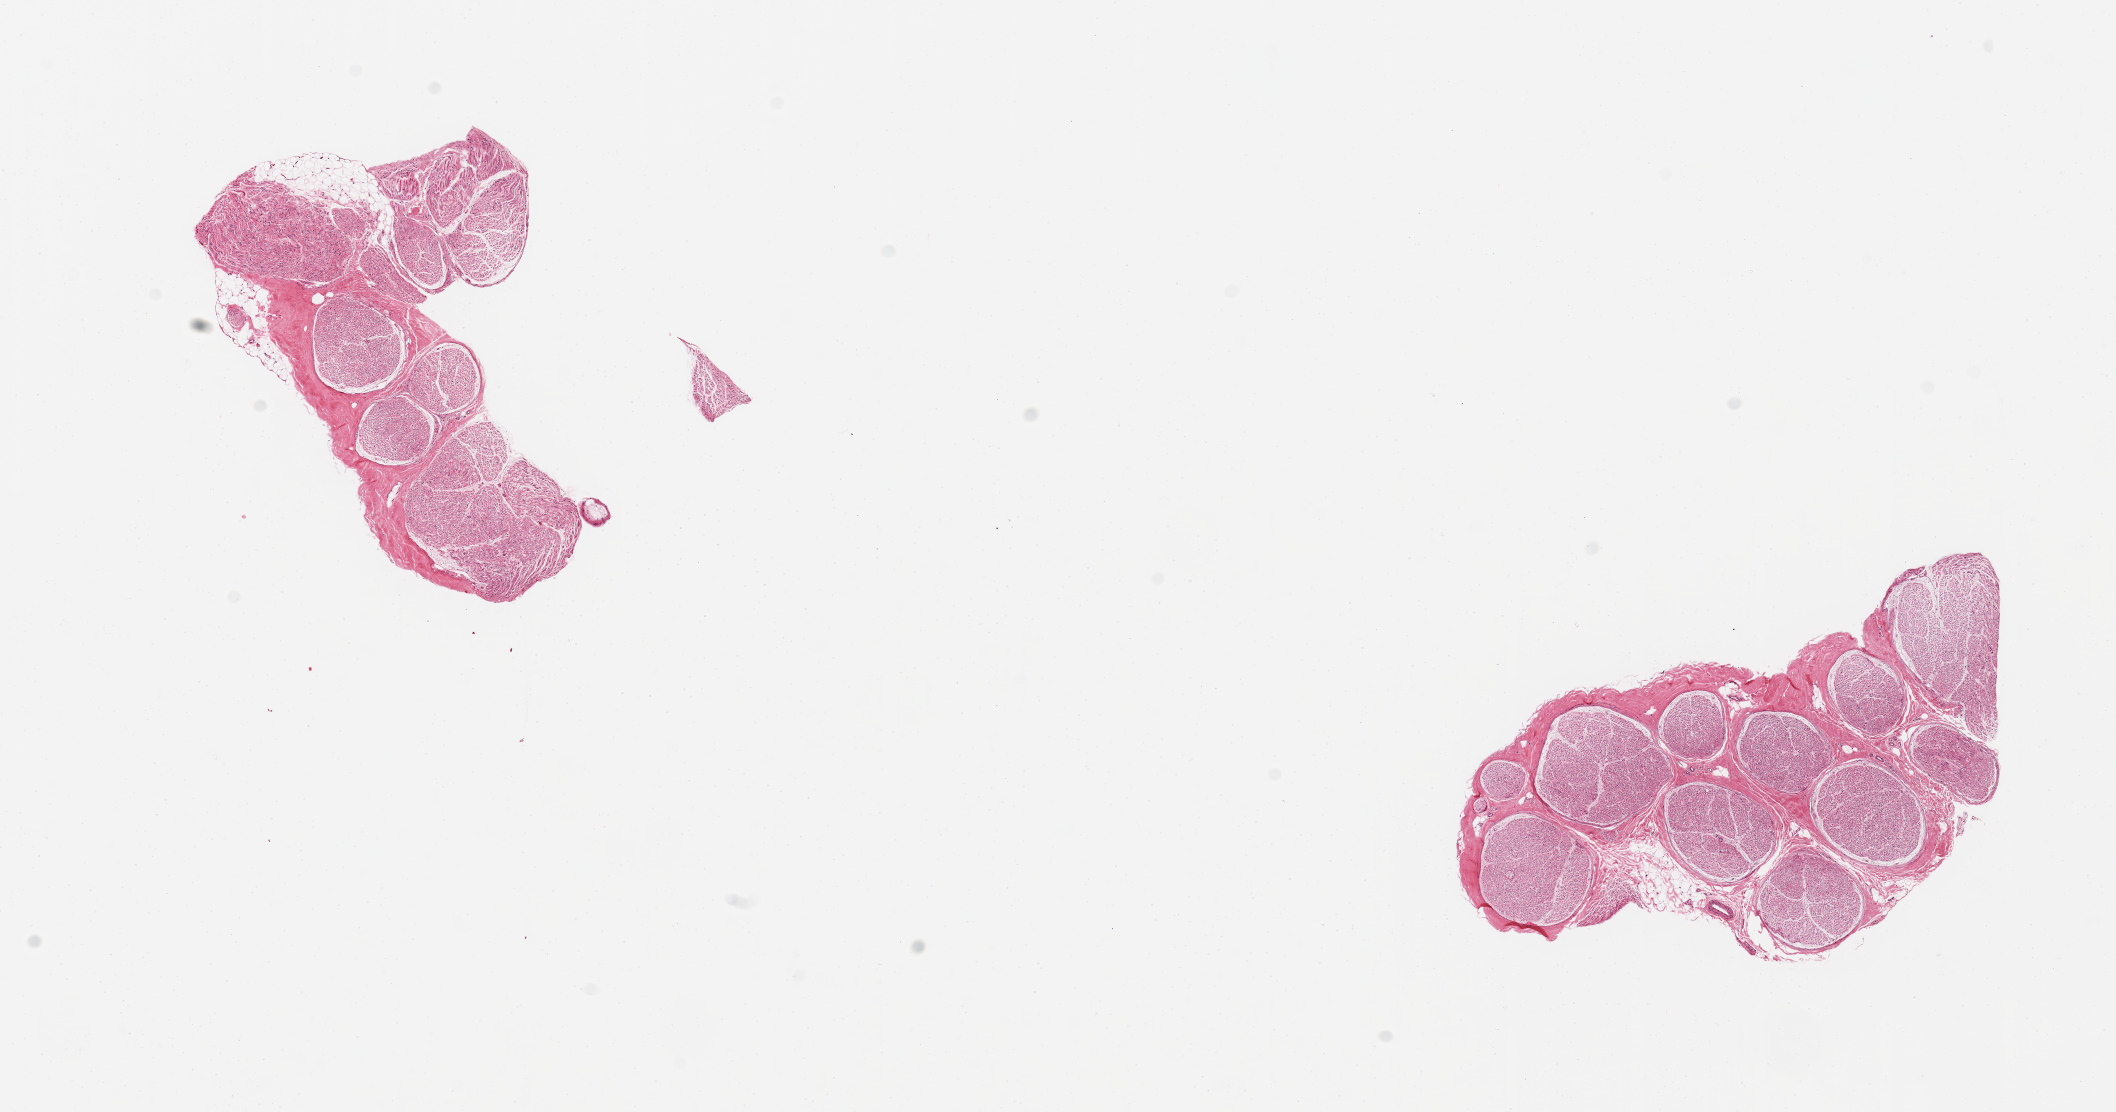
Digitized hematoxylin and eosin (H&E)-stained section, low-resolution overview of the scanned area, about 16.7 x 8.8 mm, PAXgene-fixed paraffin-embedded (PFPE) section, section of tibial nerve (target tissue), tissue donor sample. Male donor.
Review note (as recorded): 2 pieces; >5% of external fat.